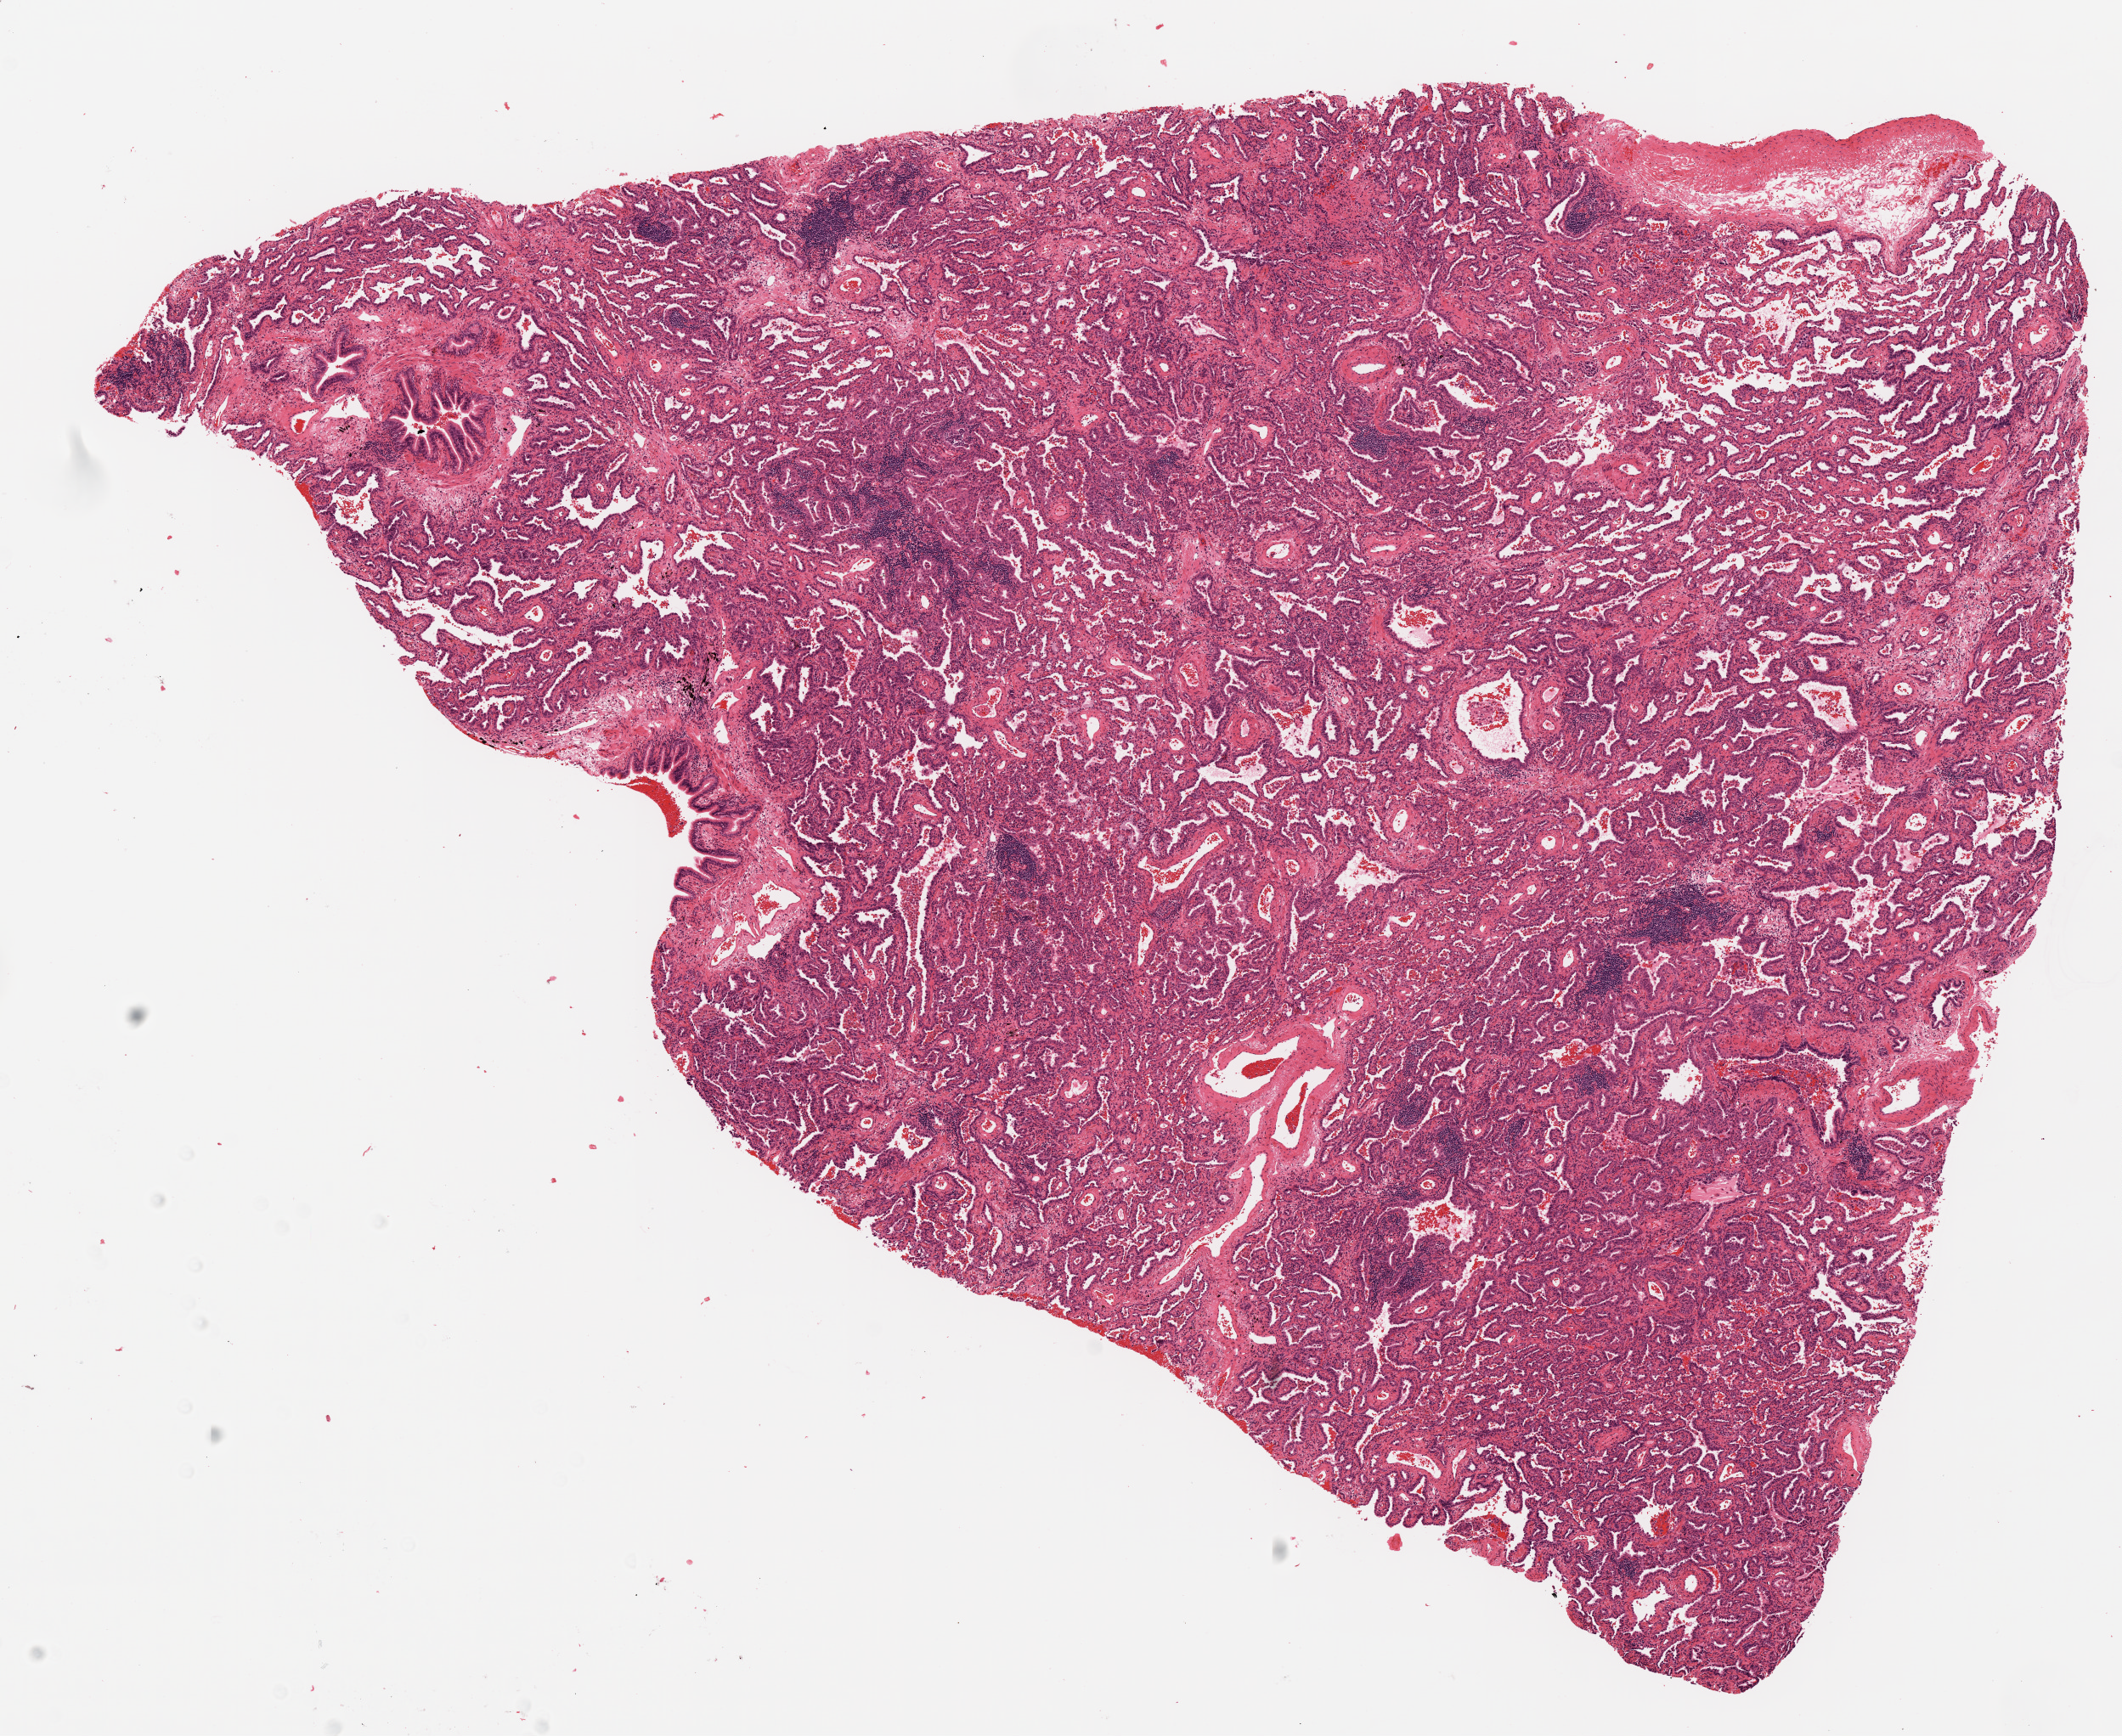
Hematoxylin and eosin (H&E) stained whole-slide image, shown as a low-resolution overview of the whole scanned area (about 10.0 x 8.2 mm, acquisition: 20x scan), FFPE section, primary tumour sample from the lung. Male patient.
- AJCC pathologic stage: IB
- pathologic diagnosis: Bronchiolo-alveolar carcinoma, non-mucinous (lower lobe, lung)
- laterality: right